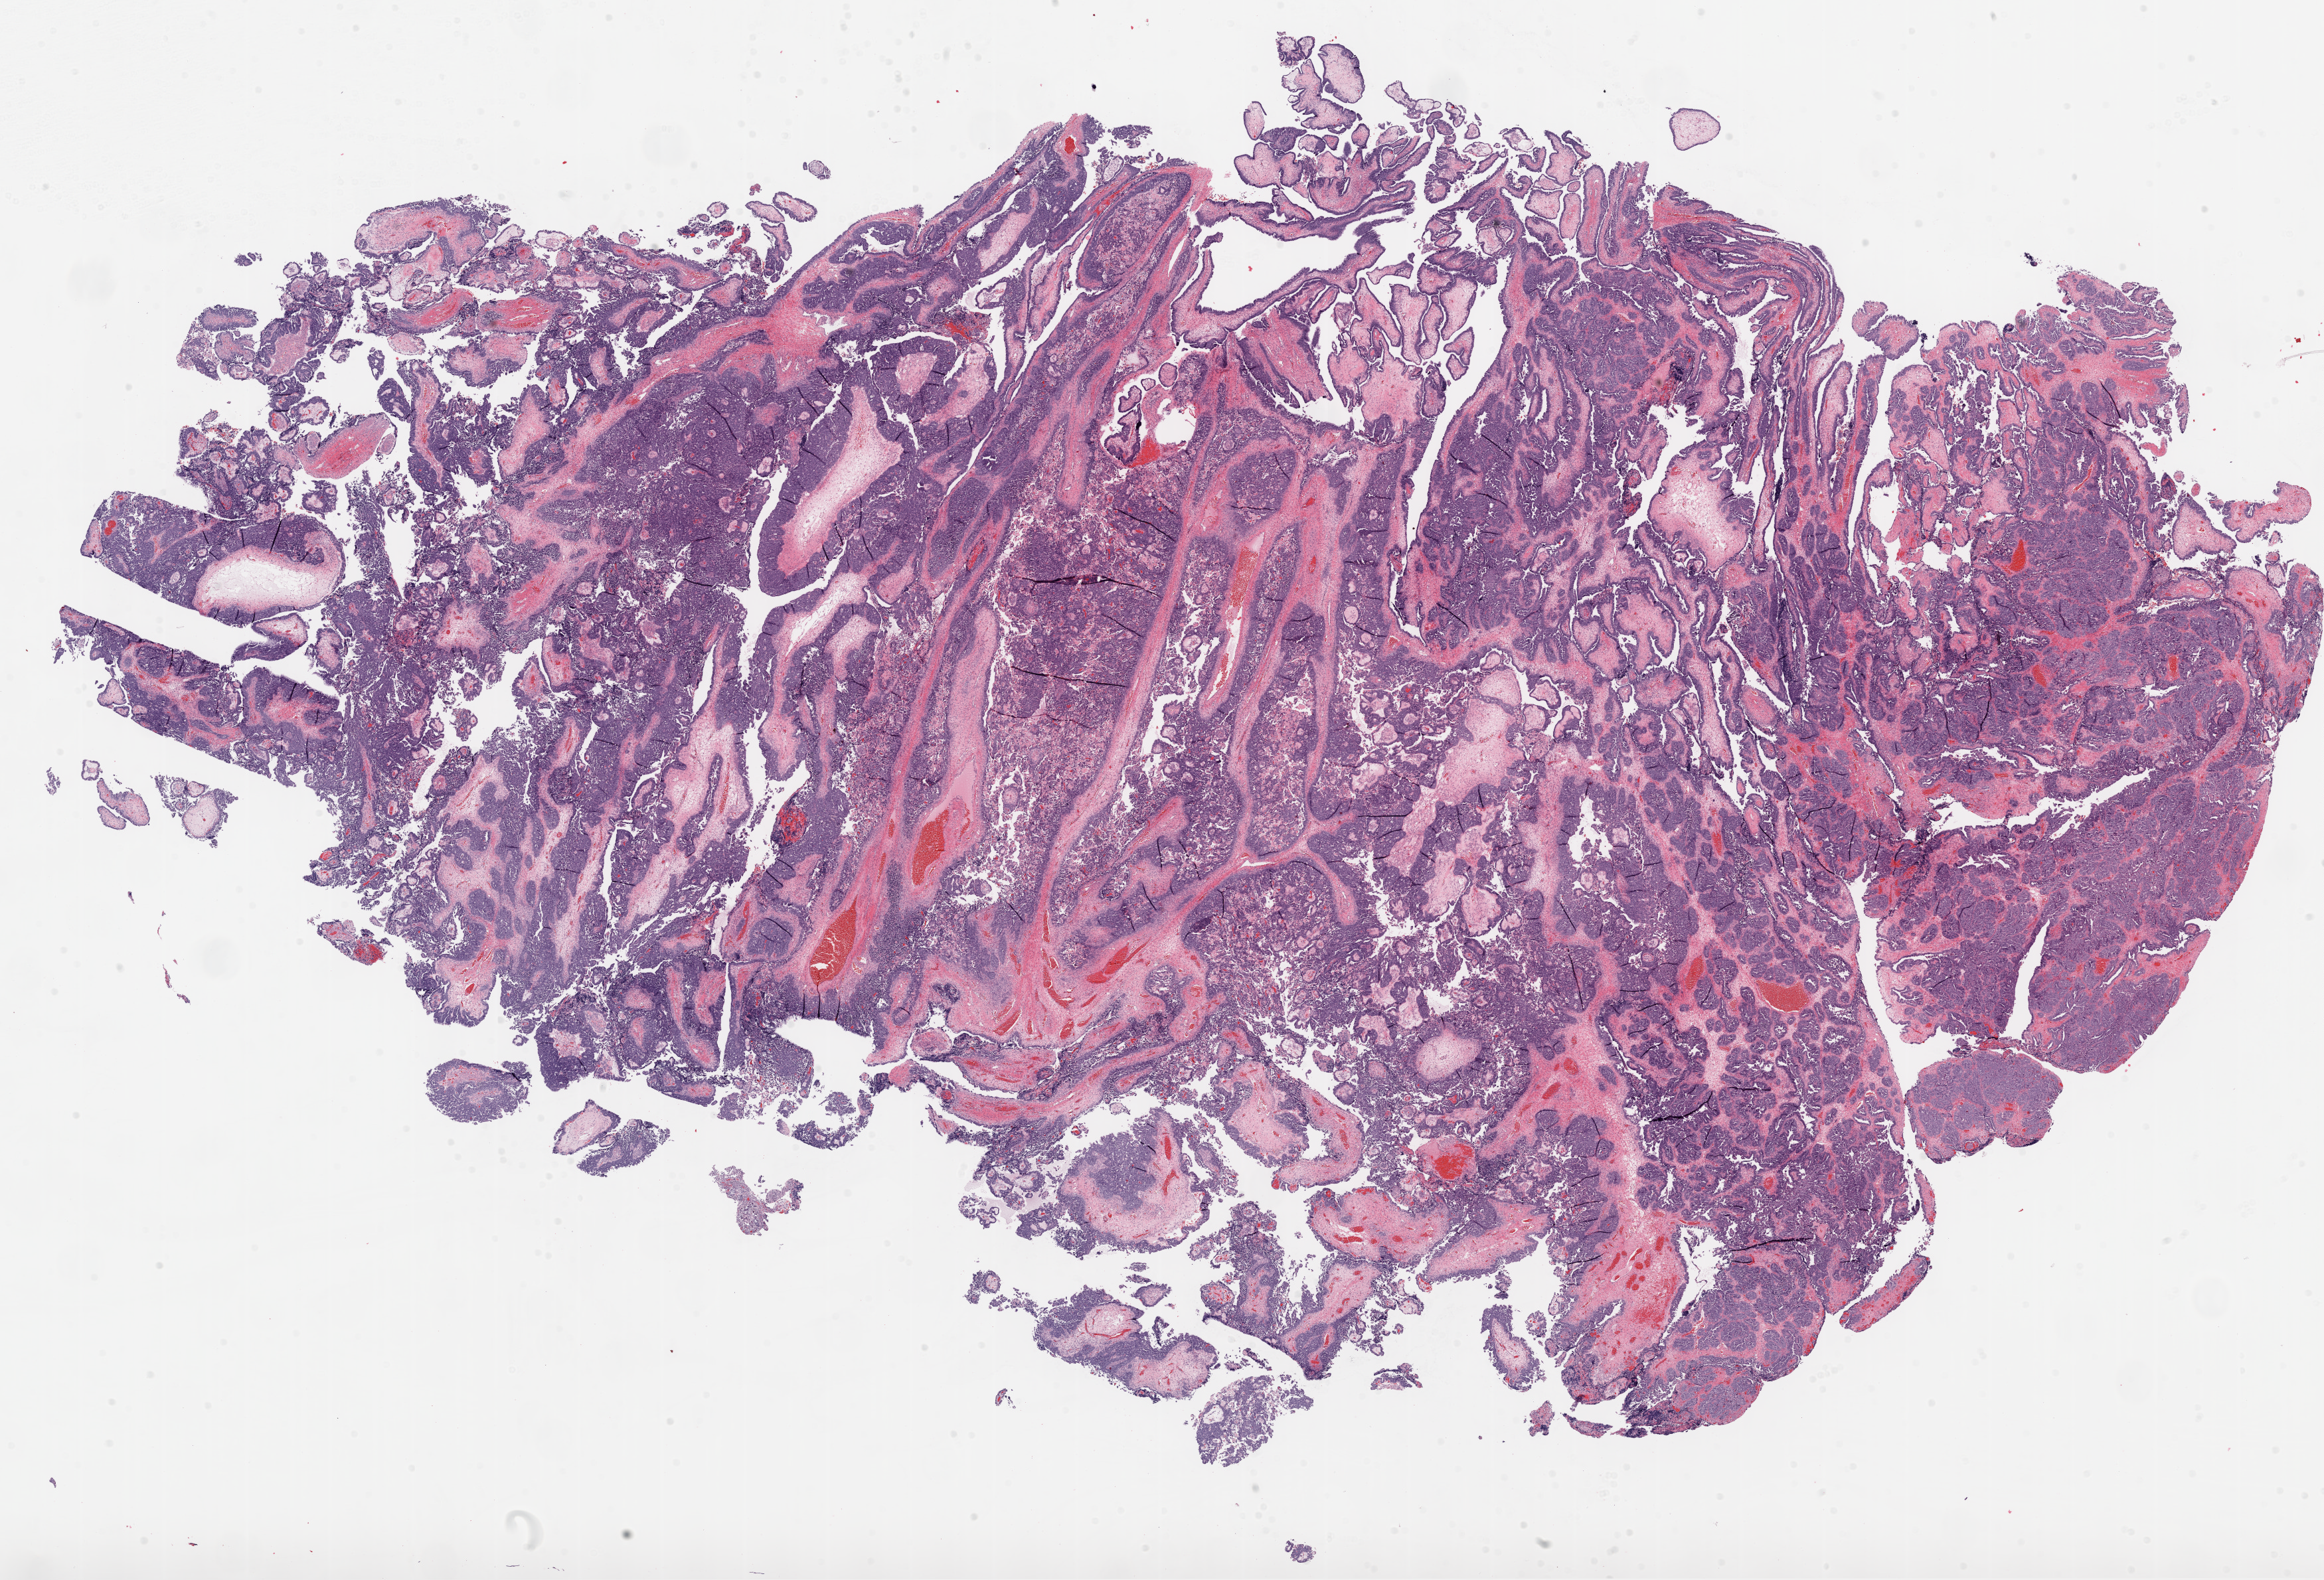
Whole-slide histology image, H&E-stained — shown as a low-resolution overview of the whole scanned area (about 28.1 x 19.1 mm, slide scanned at 20x), frozen section, primary tumour sample from the ovary. Female, age 64 years at initial diagnosis. Histologic grade: G3 (poorly differentiated). Slide review estimates, as recorded: tumour cells 67%, tumour nuclei 70%, normal cells 0%, stromal cells 30%, necrosis 3%.
Laterality: bilateral. FIGO stage: IIC. Pathologic diagnosis: Serous cystadenocarcinoma, NOS.